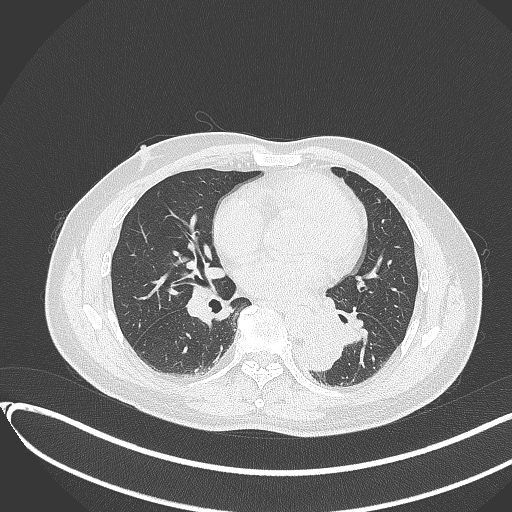
Chest CT, one axial slice. Slice 156 of 417 in the series (ordered by position). Reconstruction kernel B70f. 120 kVp. Lung window (W 1500 / L -600 HU). 512 × 512 image matrix, field of view 400 × 400 mm. Patient: male, 54 years. From the clinical record (not read from this slice): clinical TNM (as recorded): T3 N0 M0.
Outlined on this slice (bounding box drawn by a radiologist):
- lung tumour (recorded histology: squamous cell carcinoma): bounding box (x1, y1, x2, y2) in pixels: (297, 332, 346, 375)